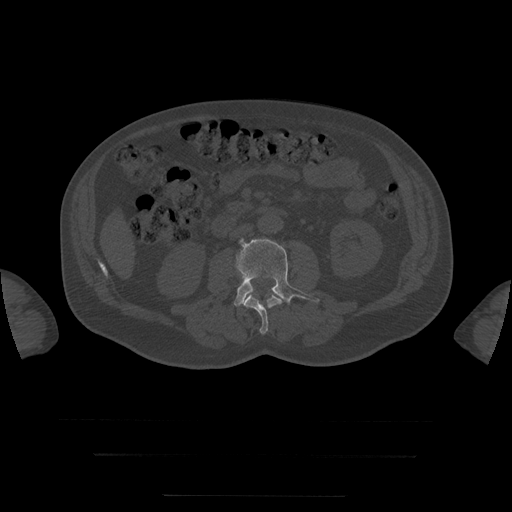
CT including the spine, one axial slice; position 6 of 397 along the scan axis; reconstruction kernel STANDARD; 120 kVp; bone window (W 1800 / L 400 HU); 1.25 mm slice thickness; 512 × 512 image matrix, field of view 510 × 510 mm. Patient age 73 years. Case-level facts recorded for this patient, not image findings: primary cancer: prostate.
Outlined on this slice (semi-automatically segmented with operator editing):
- L3 vertebra: bounding box [x1, y1, x2, y2] px = [234, 239, 320, 306]